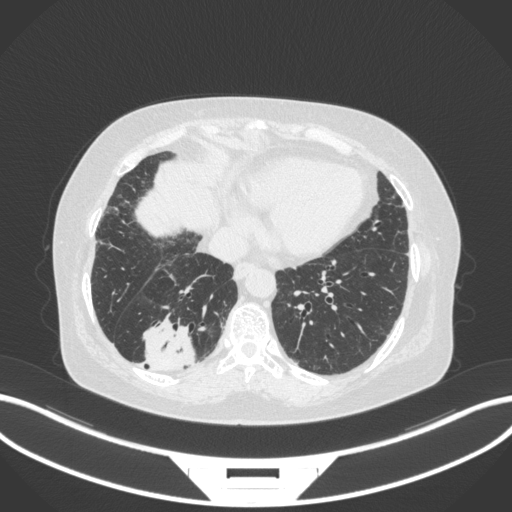
Chest CT, one axial slice; slice 62 of 303 in the series (ordered by position); lung window (W 1500 / L -600 HU); 512 × 512 image matrix, field of view 400 × 400 mm. Patient: female, 65 years. From the clinical record (not read from this slice): clinical TNM (as recorded): T2b N1 M0.
Annotated regions visible in this slice (bounding box drawn by a radiologist):
- lung tumour (recorded histology: adenocarcinoma): bounding box (x1, y1, x2, y2) in pixels: (138, 315, 199, 375)